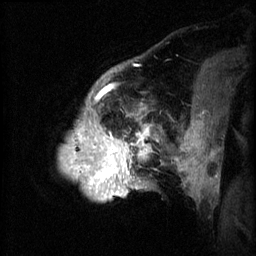
Breast MRI (dynamic contrast-enhanced), one sagittal slice; slice 10 of 60 in the series (ordered by position); 3 images stored at this slice position (order not interpretable as contrast timing); 1.5 T; TE 4.2 ms, TR 8.2 ms; 2.3 mm slice thickness; 256 × 256 image matrix. Patient: female, 50 years.
Annotated regions visible in this slice (semi-automatic segmentation, software-assisted and operator-edited):
- analysis volume of interest (the breast-tissue region the enhancement analysis was run in; not a lesion): bounding box <62,64,169,203> (left, top, right, bottom; pixels)
- tumour enhancement mask (voxels above the 70 % enhancement threshold inside the analysis volume of interest): <66,84,153,193>